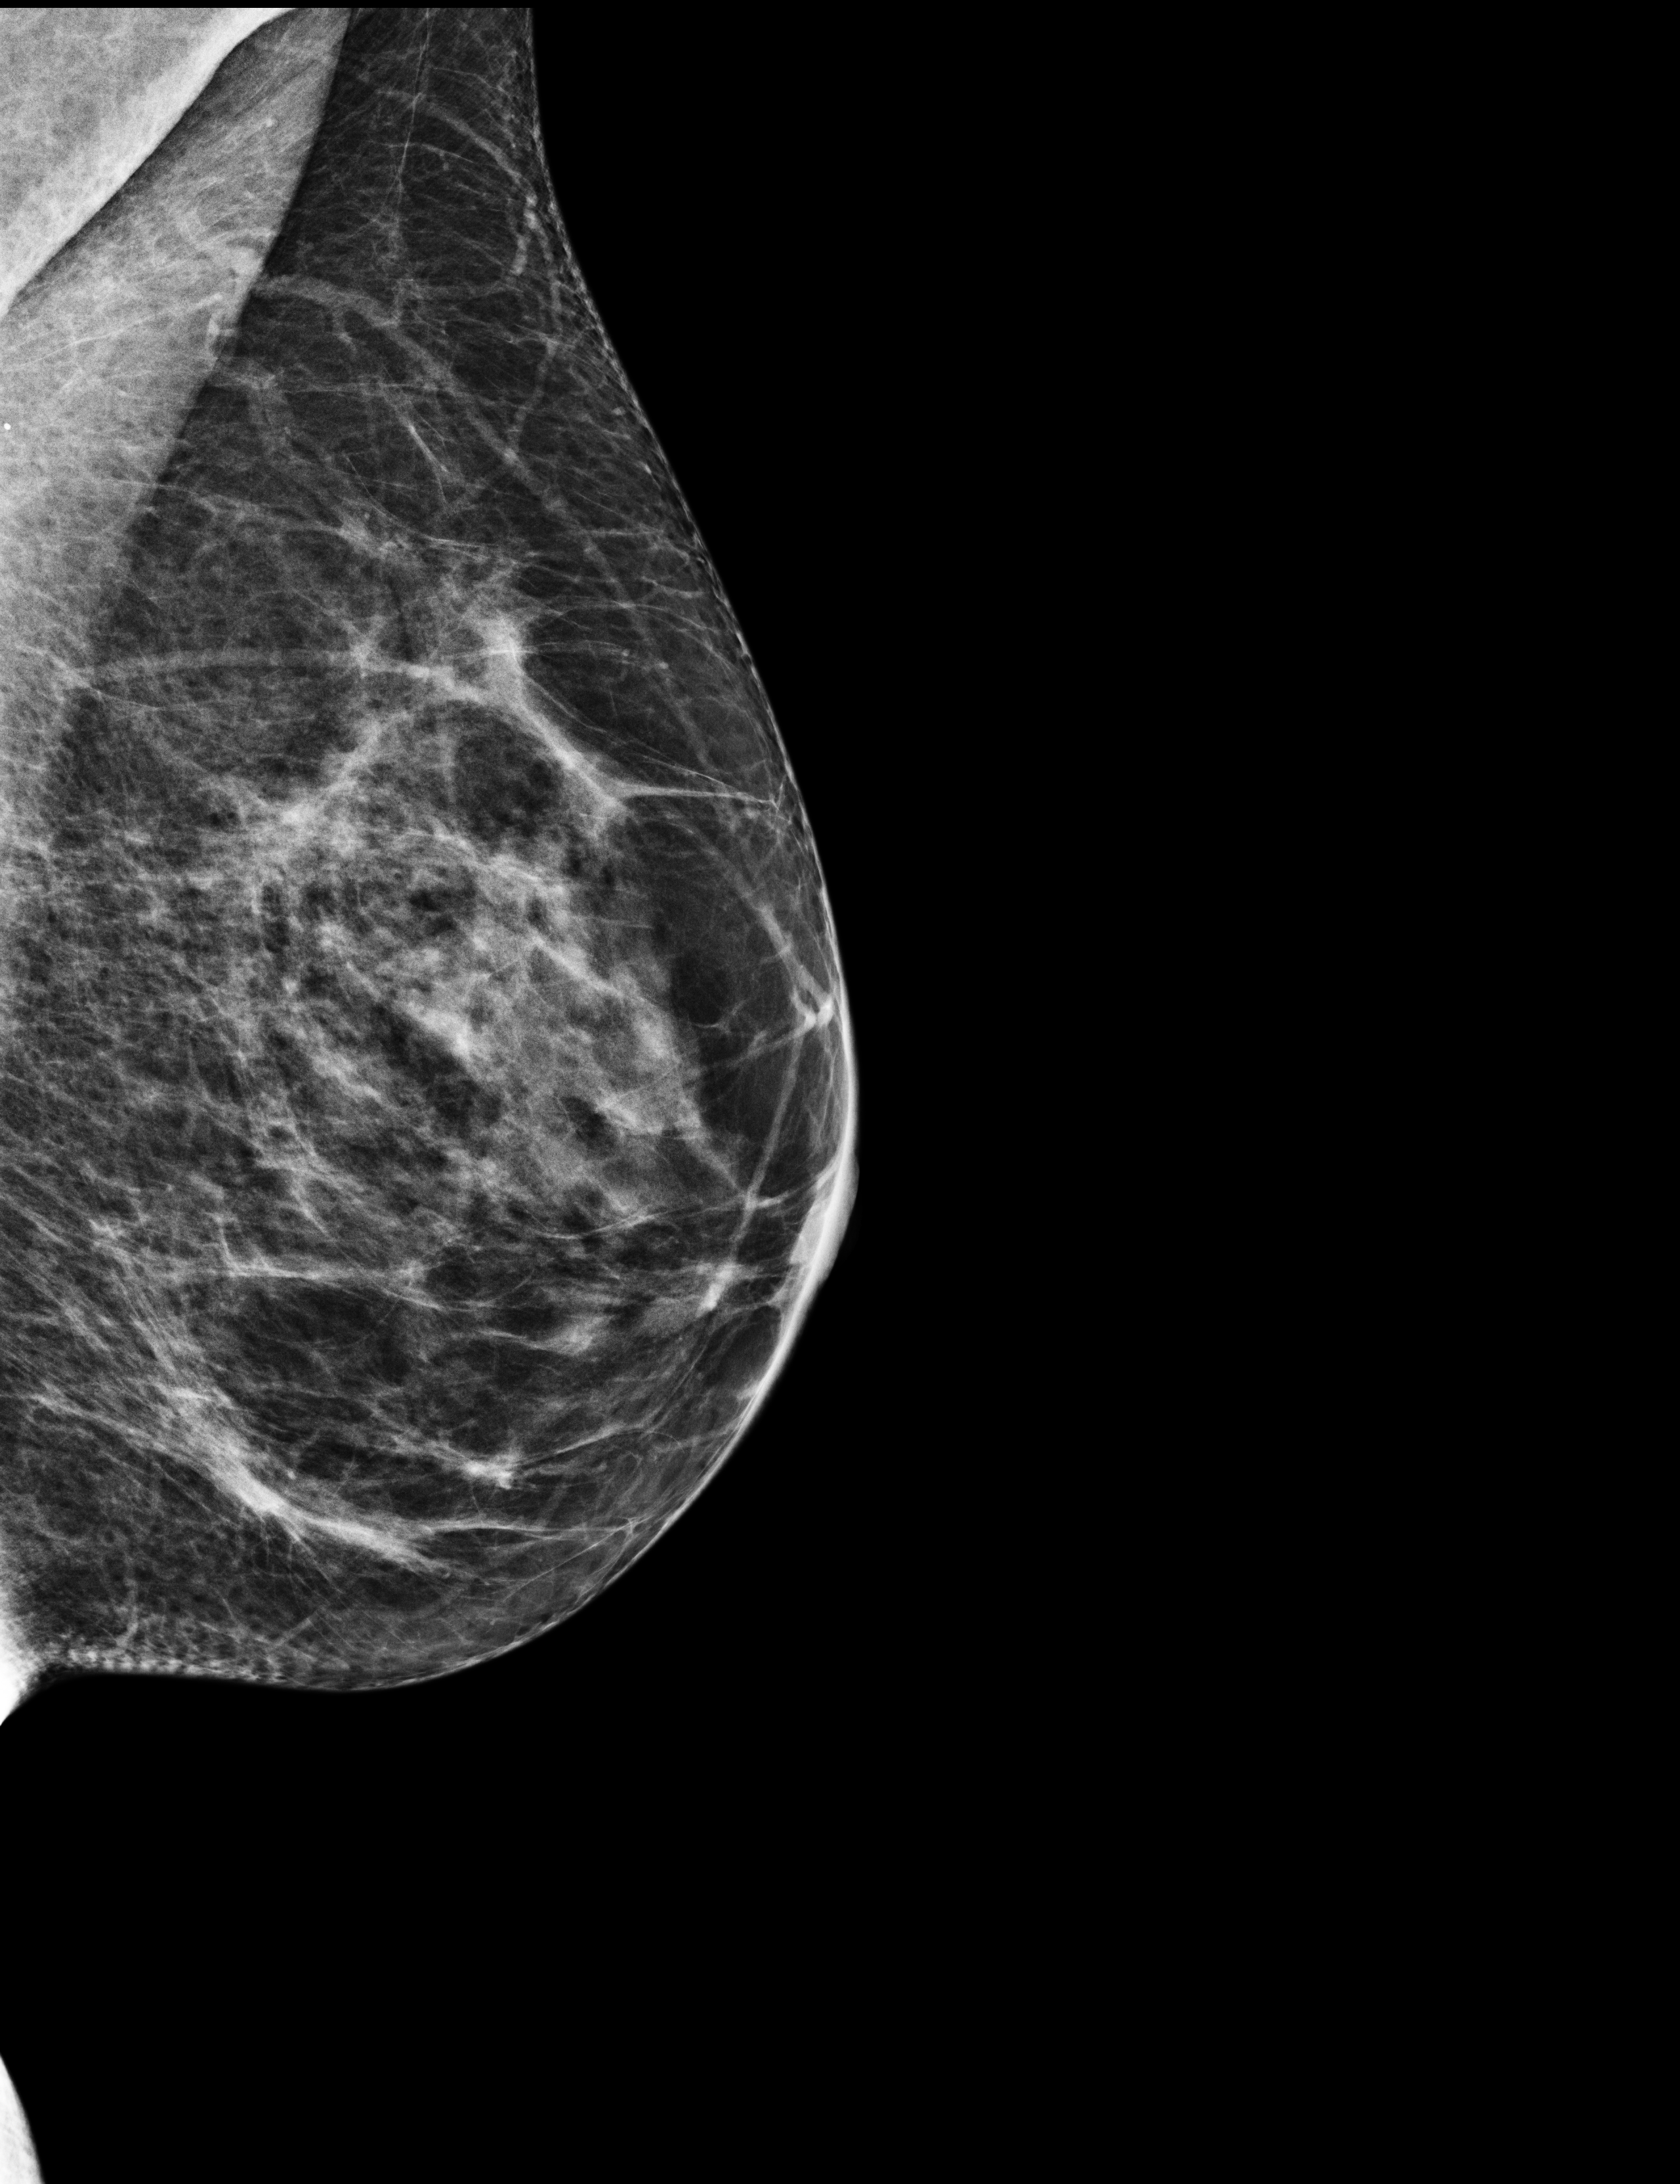
Full-field digital mammogram (FFDM); left breast; mediolateral oblique (MLO) view; annual screening mammography examination; system: Selenia Dimensions. Patient: female, 56 years.
BI-RADS breast density category at the screening exam (both breasts, scale 1–4): 3. Final BI-RADS category for the screening round (tomosynthesis exam, both breasts): category 1. Recall: no recall after this screen.